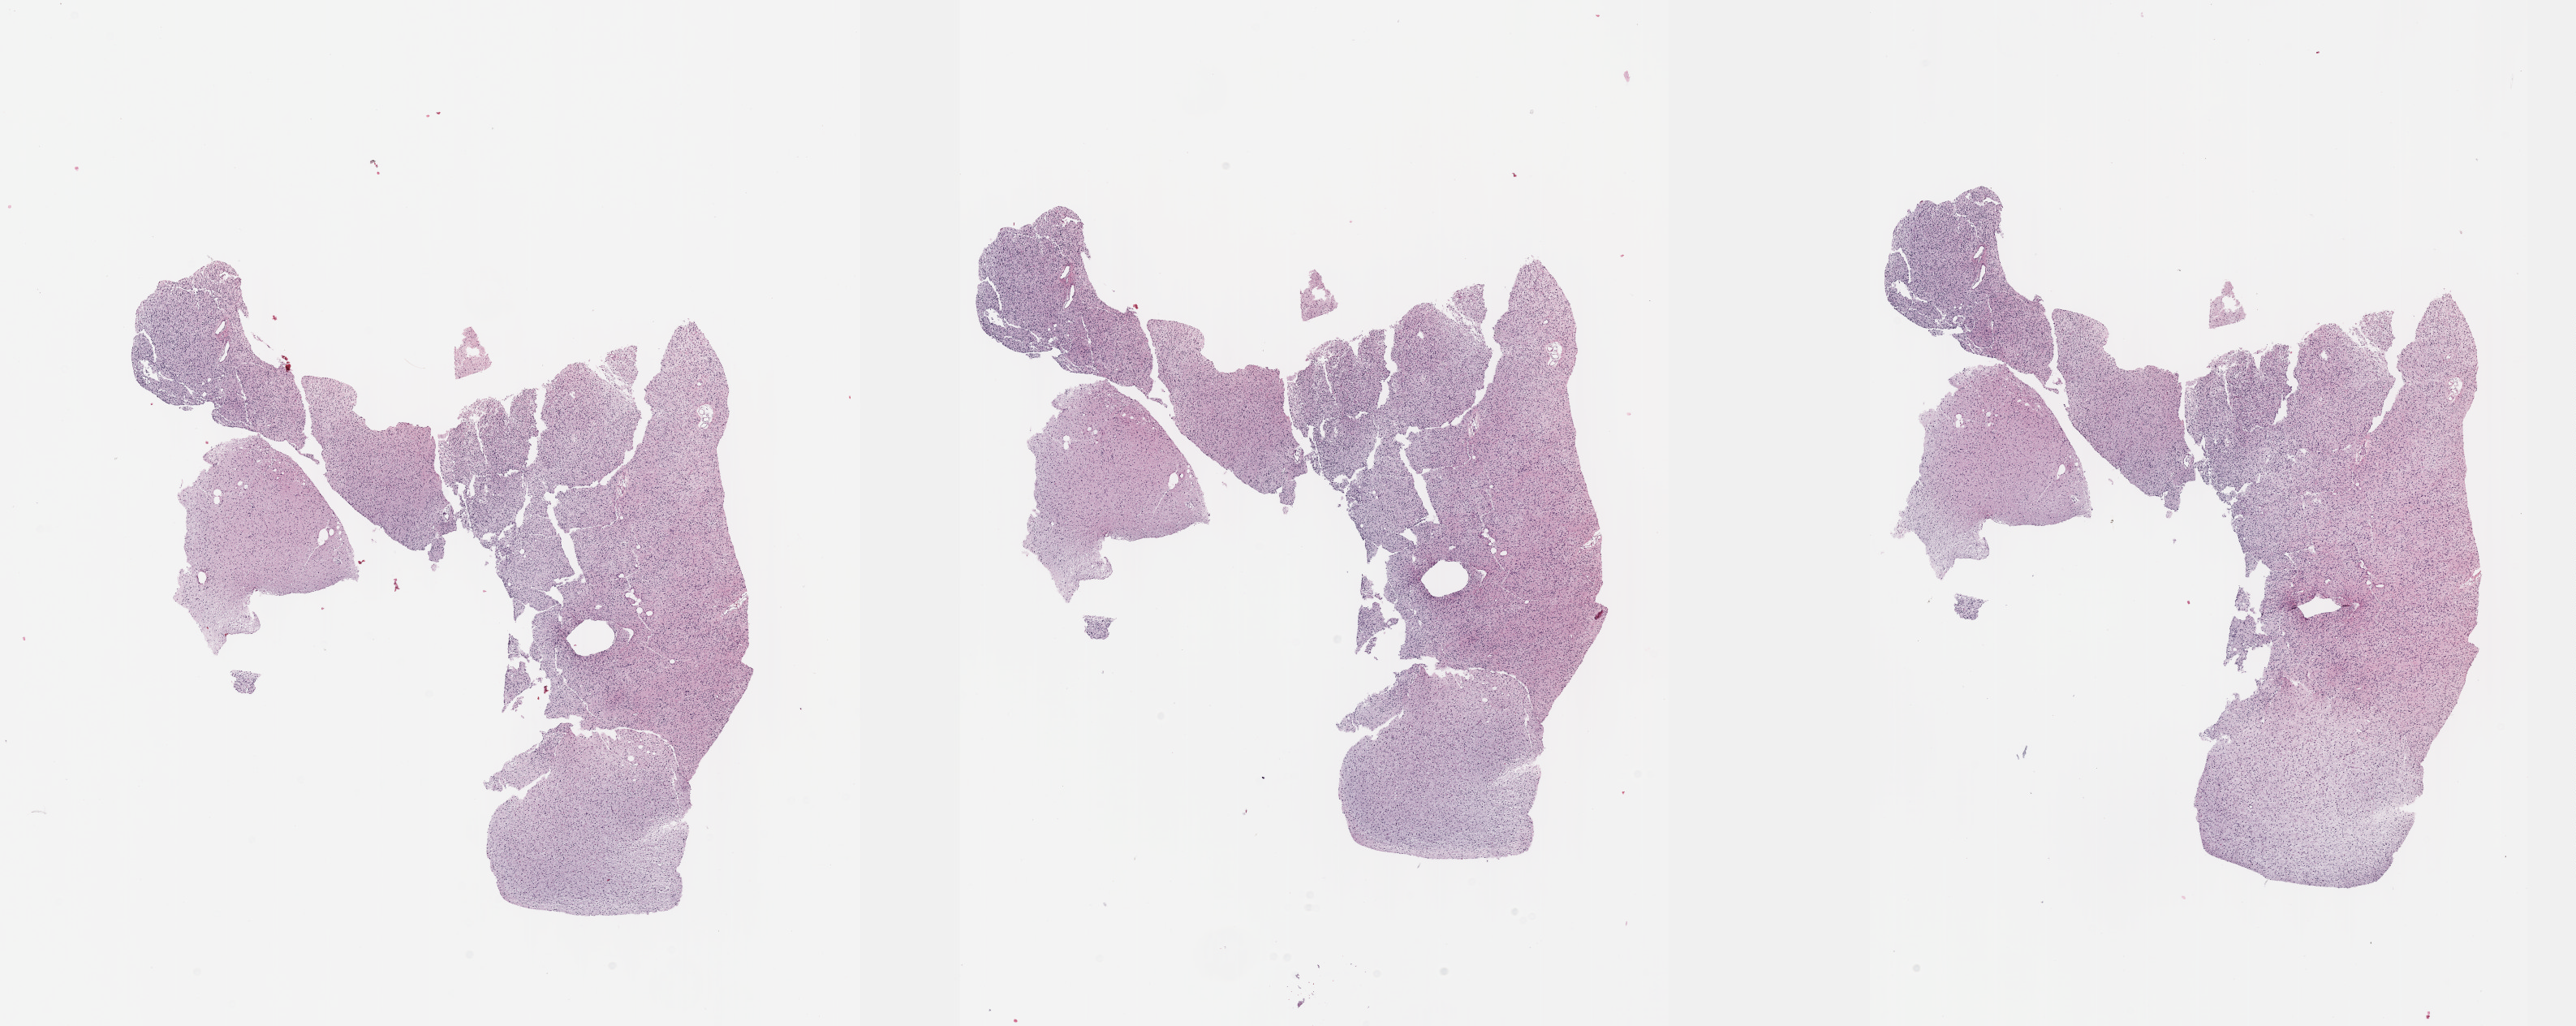
Digitized Hematoxylin and eosin (H&E) stained tissue section (whole slide), whole scanned area (about 25.7 x 10.2 mm) shown as a low-resolution overview, formalin-fixed paraffin-embedded (FFPE) diagnostic section, sample: primary tumour, brain. Male patient; age at initial diagnosis 33 years. Histologic grade: G3 (poorly differentiated).
Histologic diagnosis: Astrocytoma, anaplastic (cerebrum). Laterality: left.